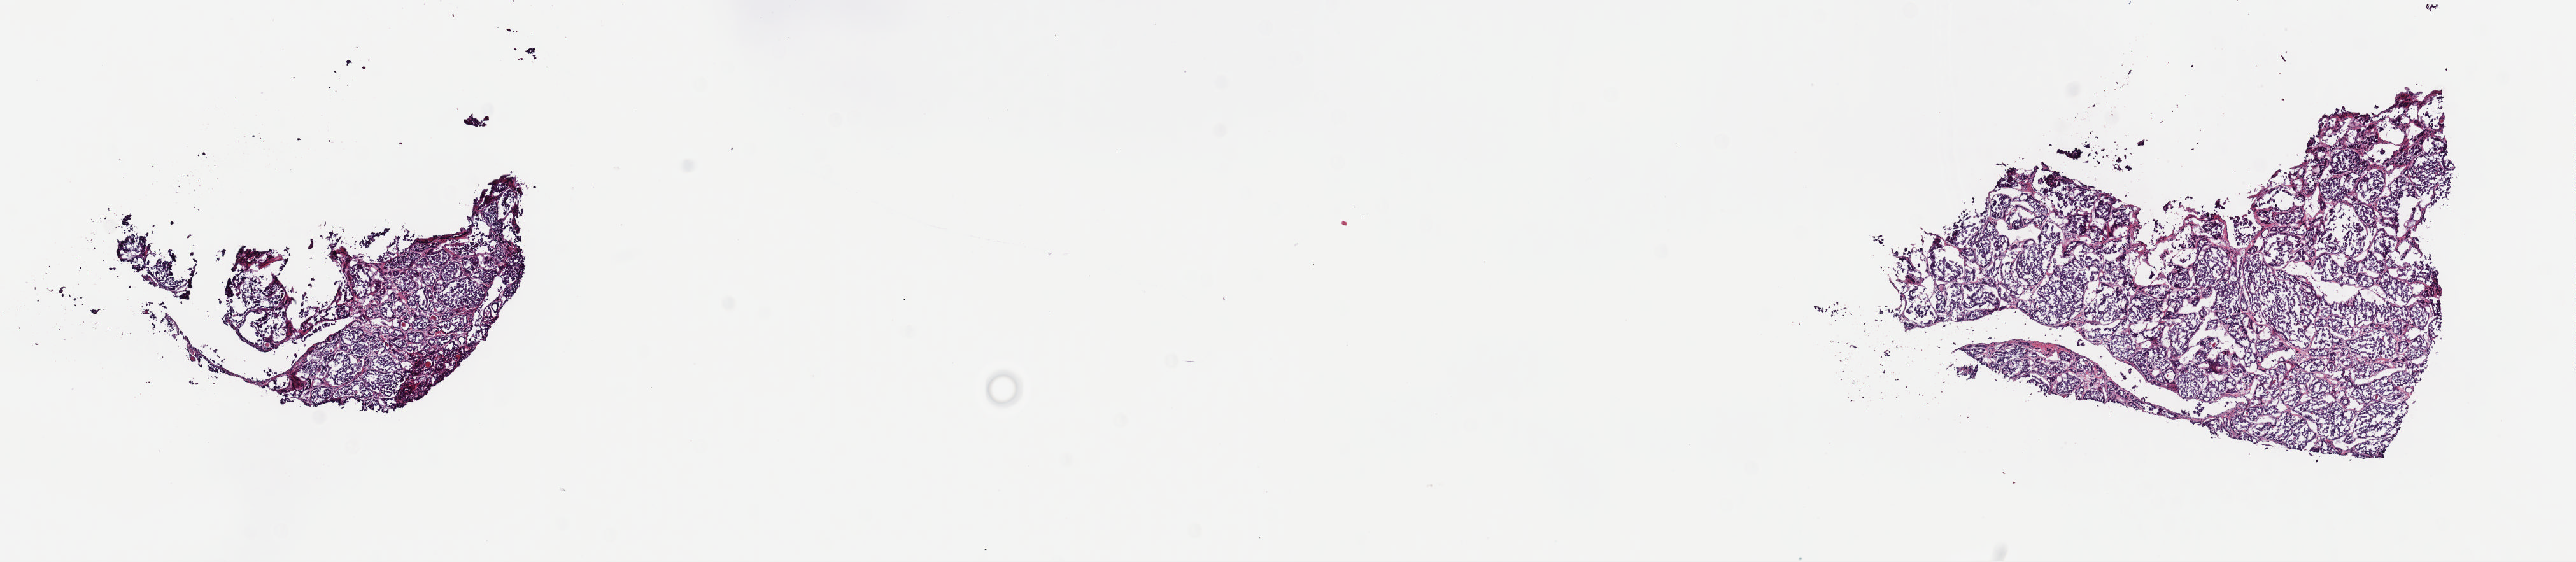
Whole-slide histology image, H&E-stained — a low-resolution overview of the entire scanned area, about 16.0 x 3.5 mm. Frozen section. Sample: primary tumour, thyroid. Male patient; age at initial diagnosis 16 years. Composition of this section per pathologist review: tumour cells 85%, tumour nuclei 100%, normal cells 0%, stromal cells 15%, necrosis 0%. Infiltration values recorded for this section: lymphocyte infiltration 0%, monocyte infiltration 0%, neutrophil infiltration 0%.
Laterality: left. Histologic diagnosis: Papillary carcinoma, follicular variant (thyroid gland). AJCC pathologic stage: II (5th edition). TNM: T4 N0 M1.